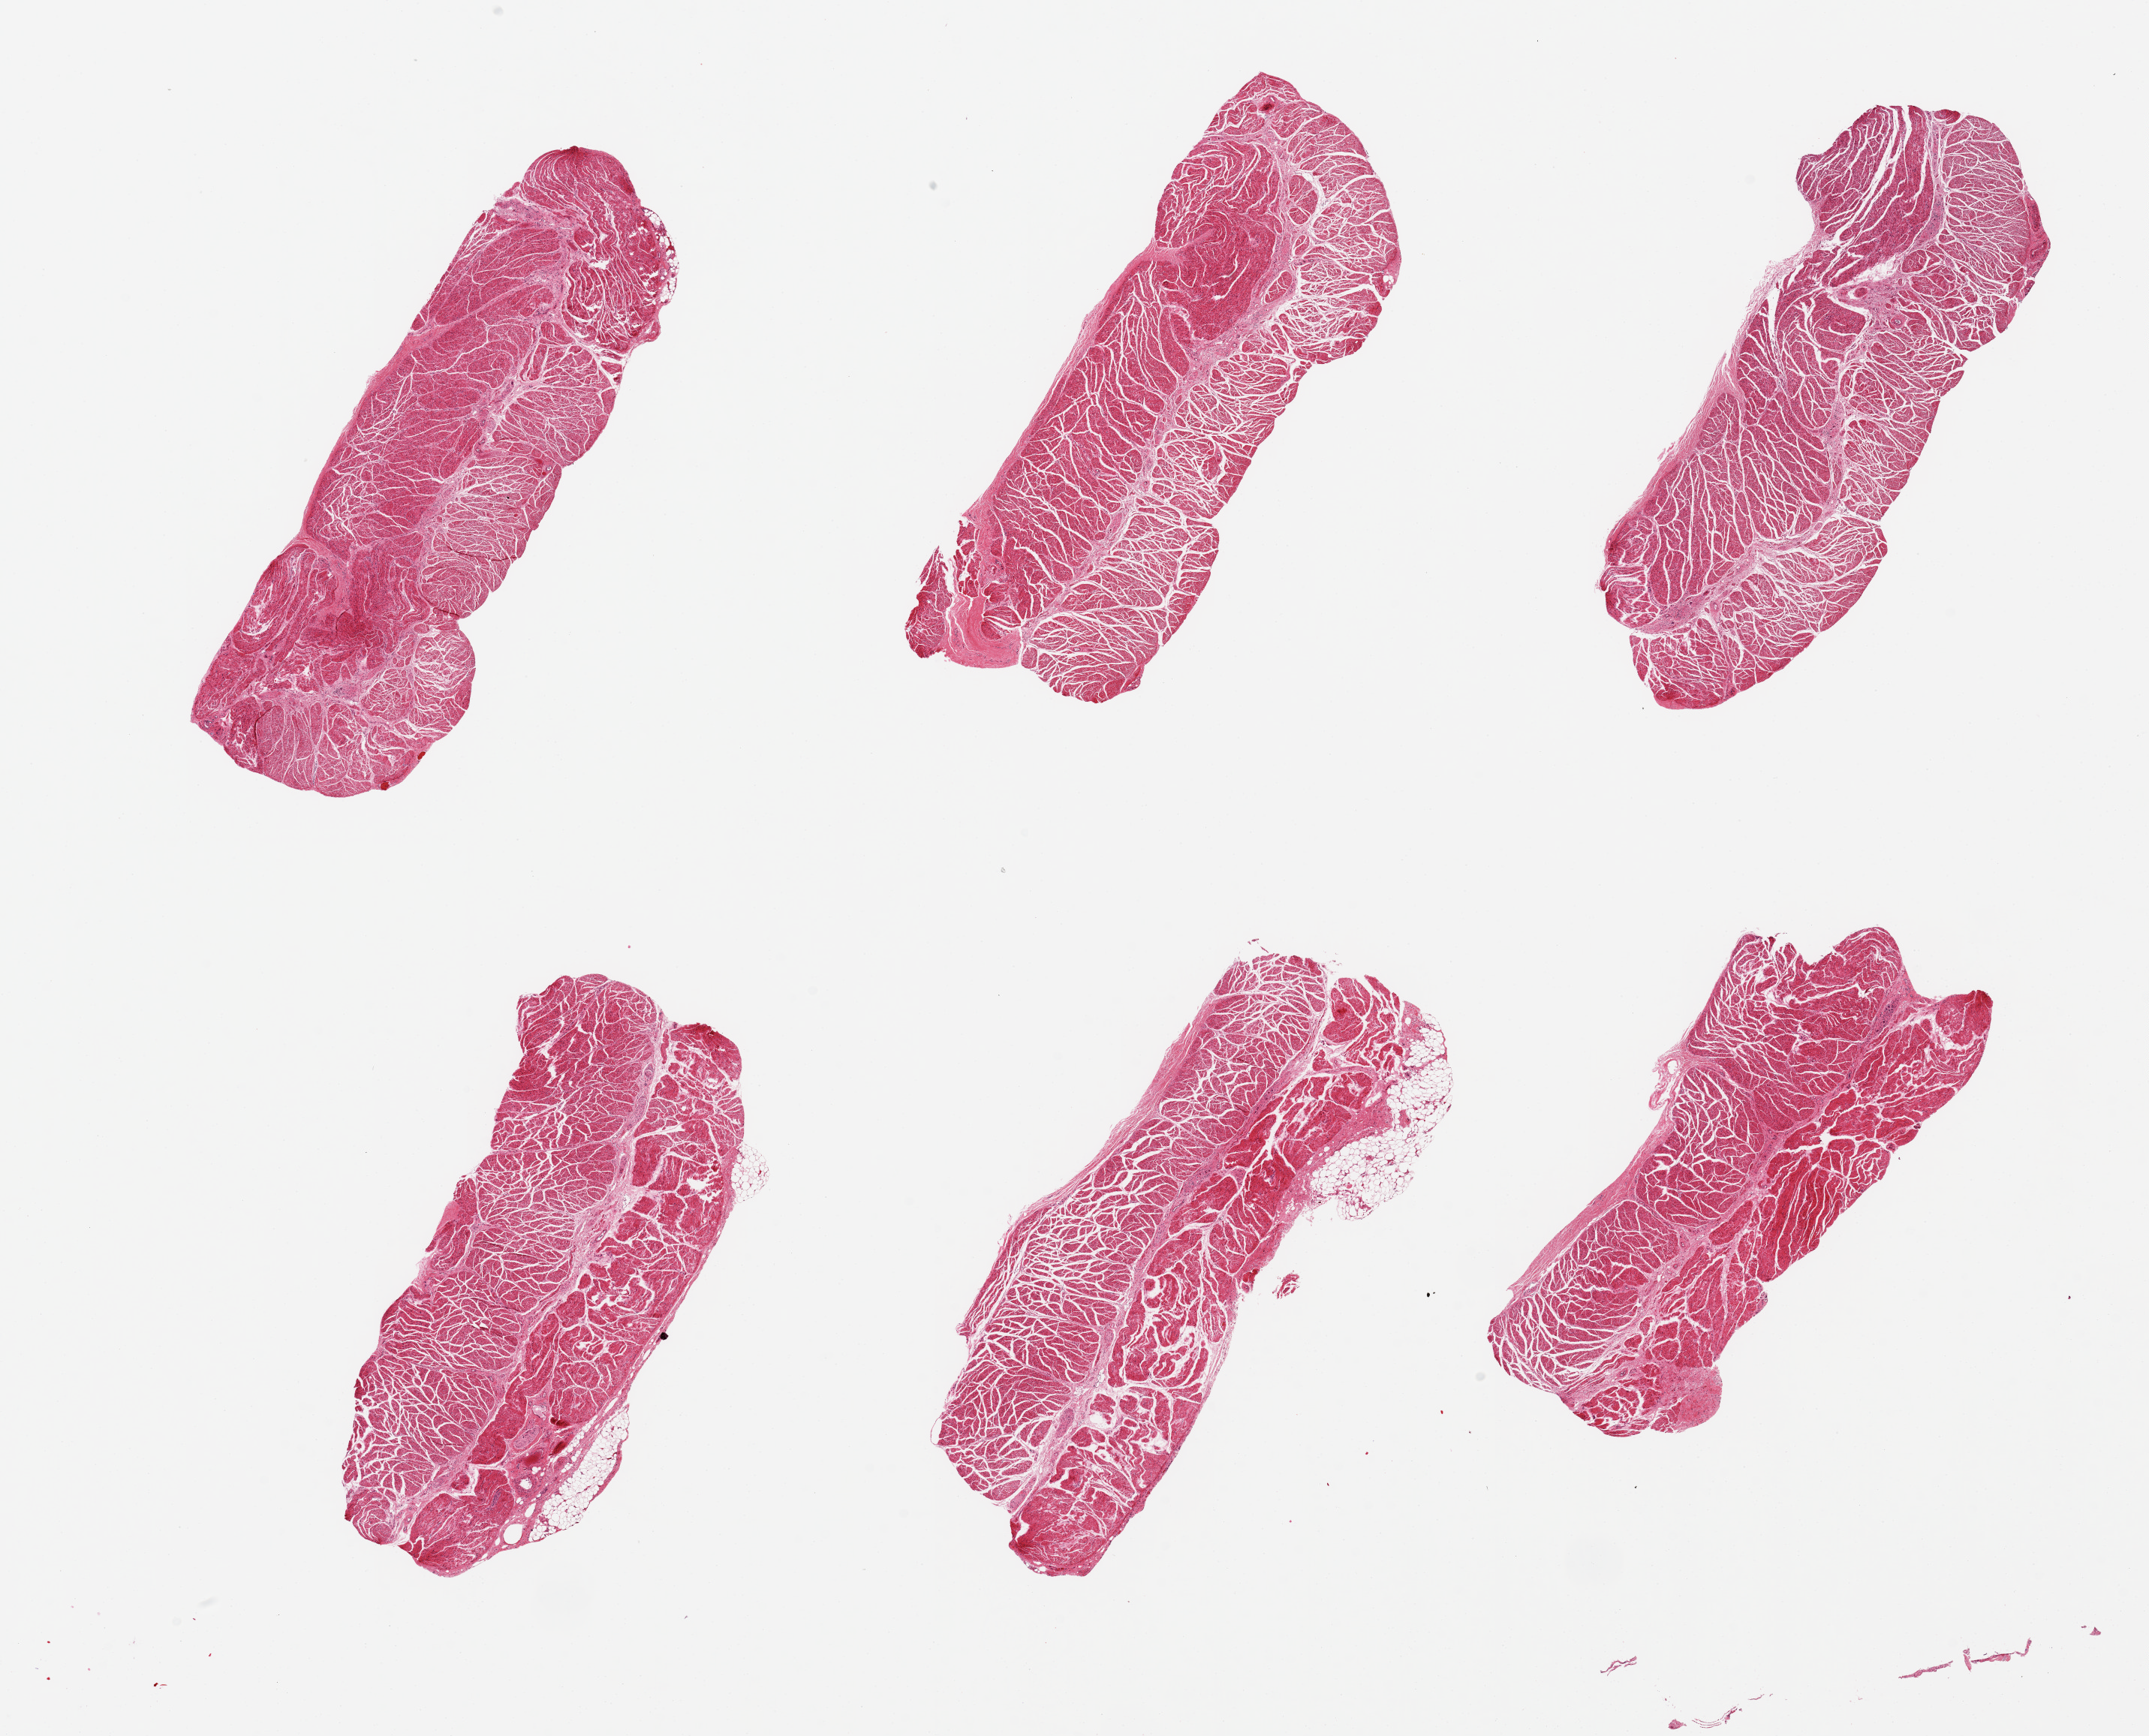
Digitized hematoxylin and eosin (H&E)-stained section, brightfield, low-resolution overview of the scanned area, about 22.6 x 18.3 mm (slide scanned at 20x); PAXgene-fixed, paraffin-embedded tissue; section of esophageal muscle (target tissue); tissue donor sample.
Pathologist's review note for this sample: 6 pieces ~~7x2mm.